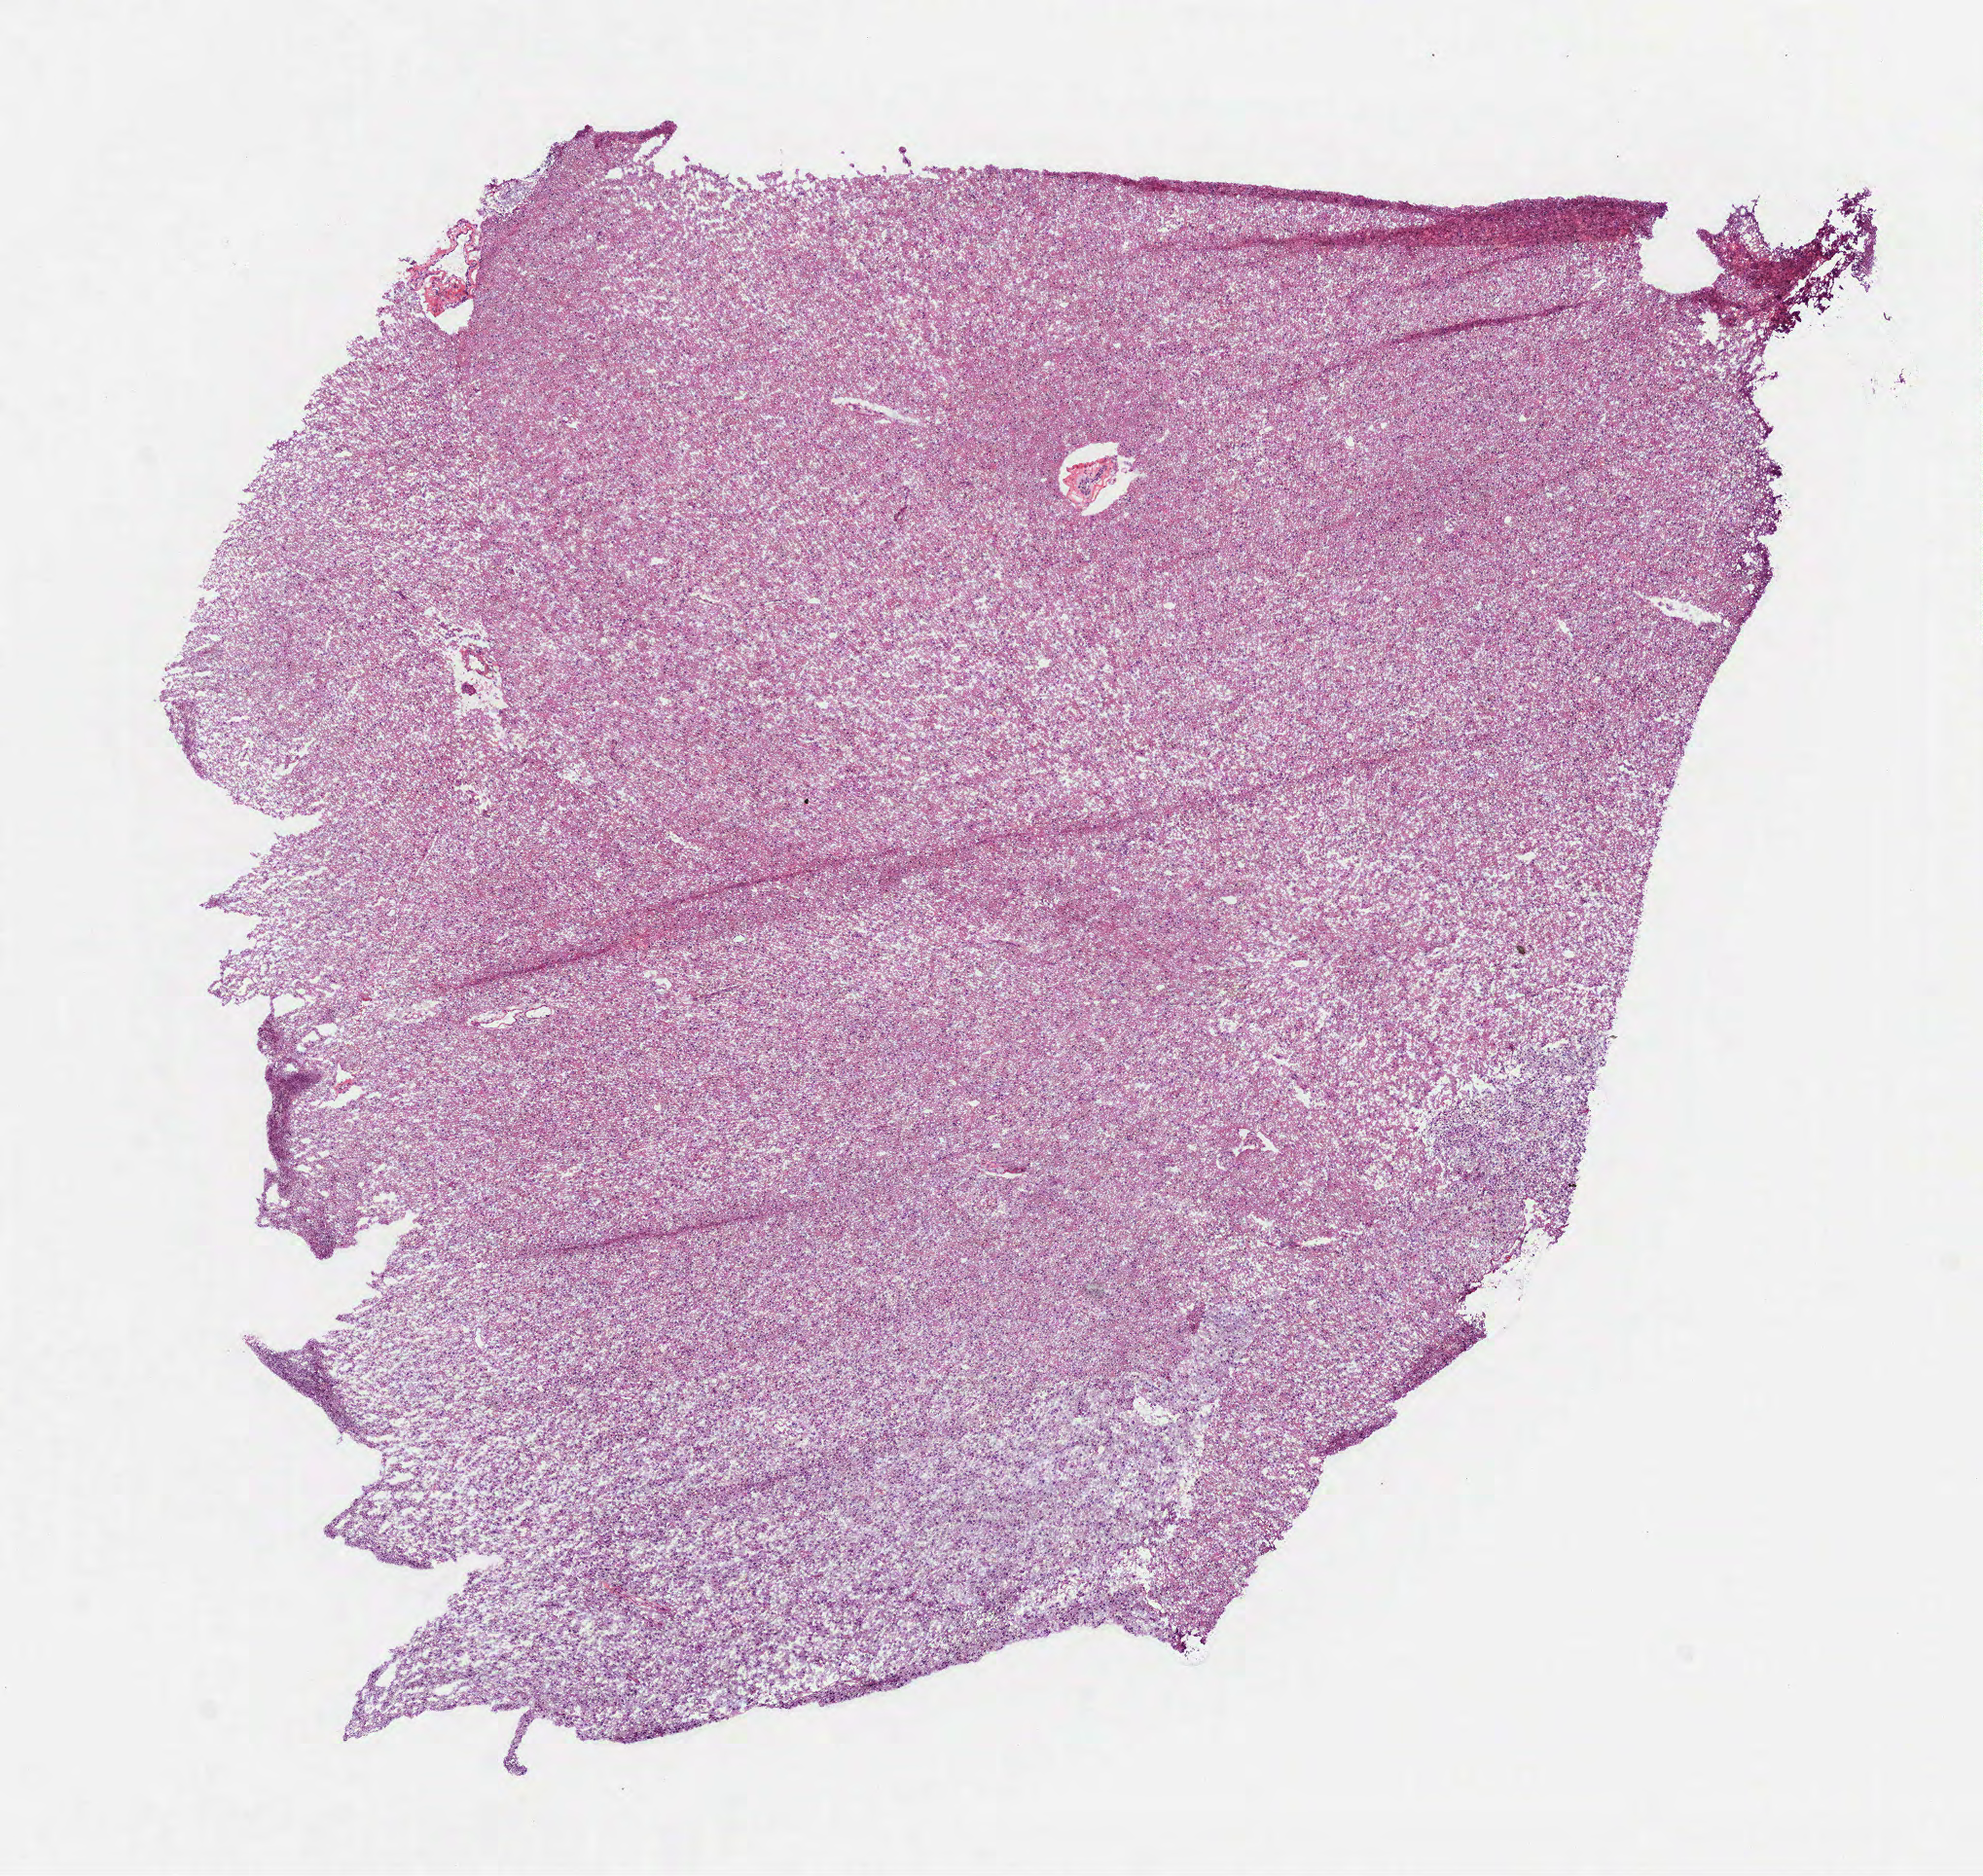
Digitized H&E-stained tissue section (whole slide), a low-resolution overview of the entire scanned area, about 8.2 x 7.8 mm, frozen section from the bottom of the tissue portion, primary tumour sample from the brain. Female patient; age at initial diagnosis 53 years. Histologic grade: G2 (moderately differentiated). Composition of this section per pathologist review: tumour cells 100%, tumour nuclei 60%, normal cells 0%, stromal cells 0%, necrosis 0%.
Pathologic diagnosis: Oligodendroglioma, NOS (cerebrum). Laterality: right.